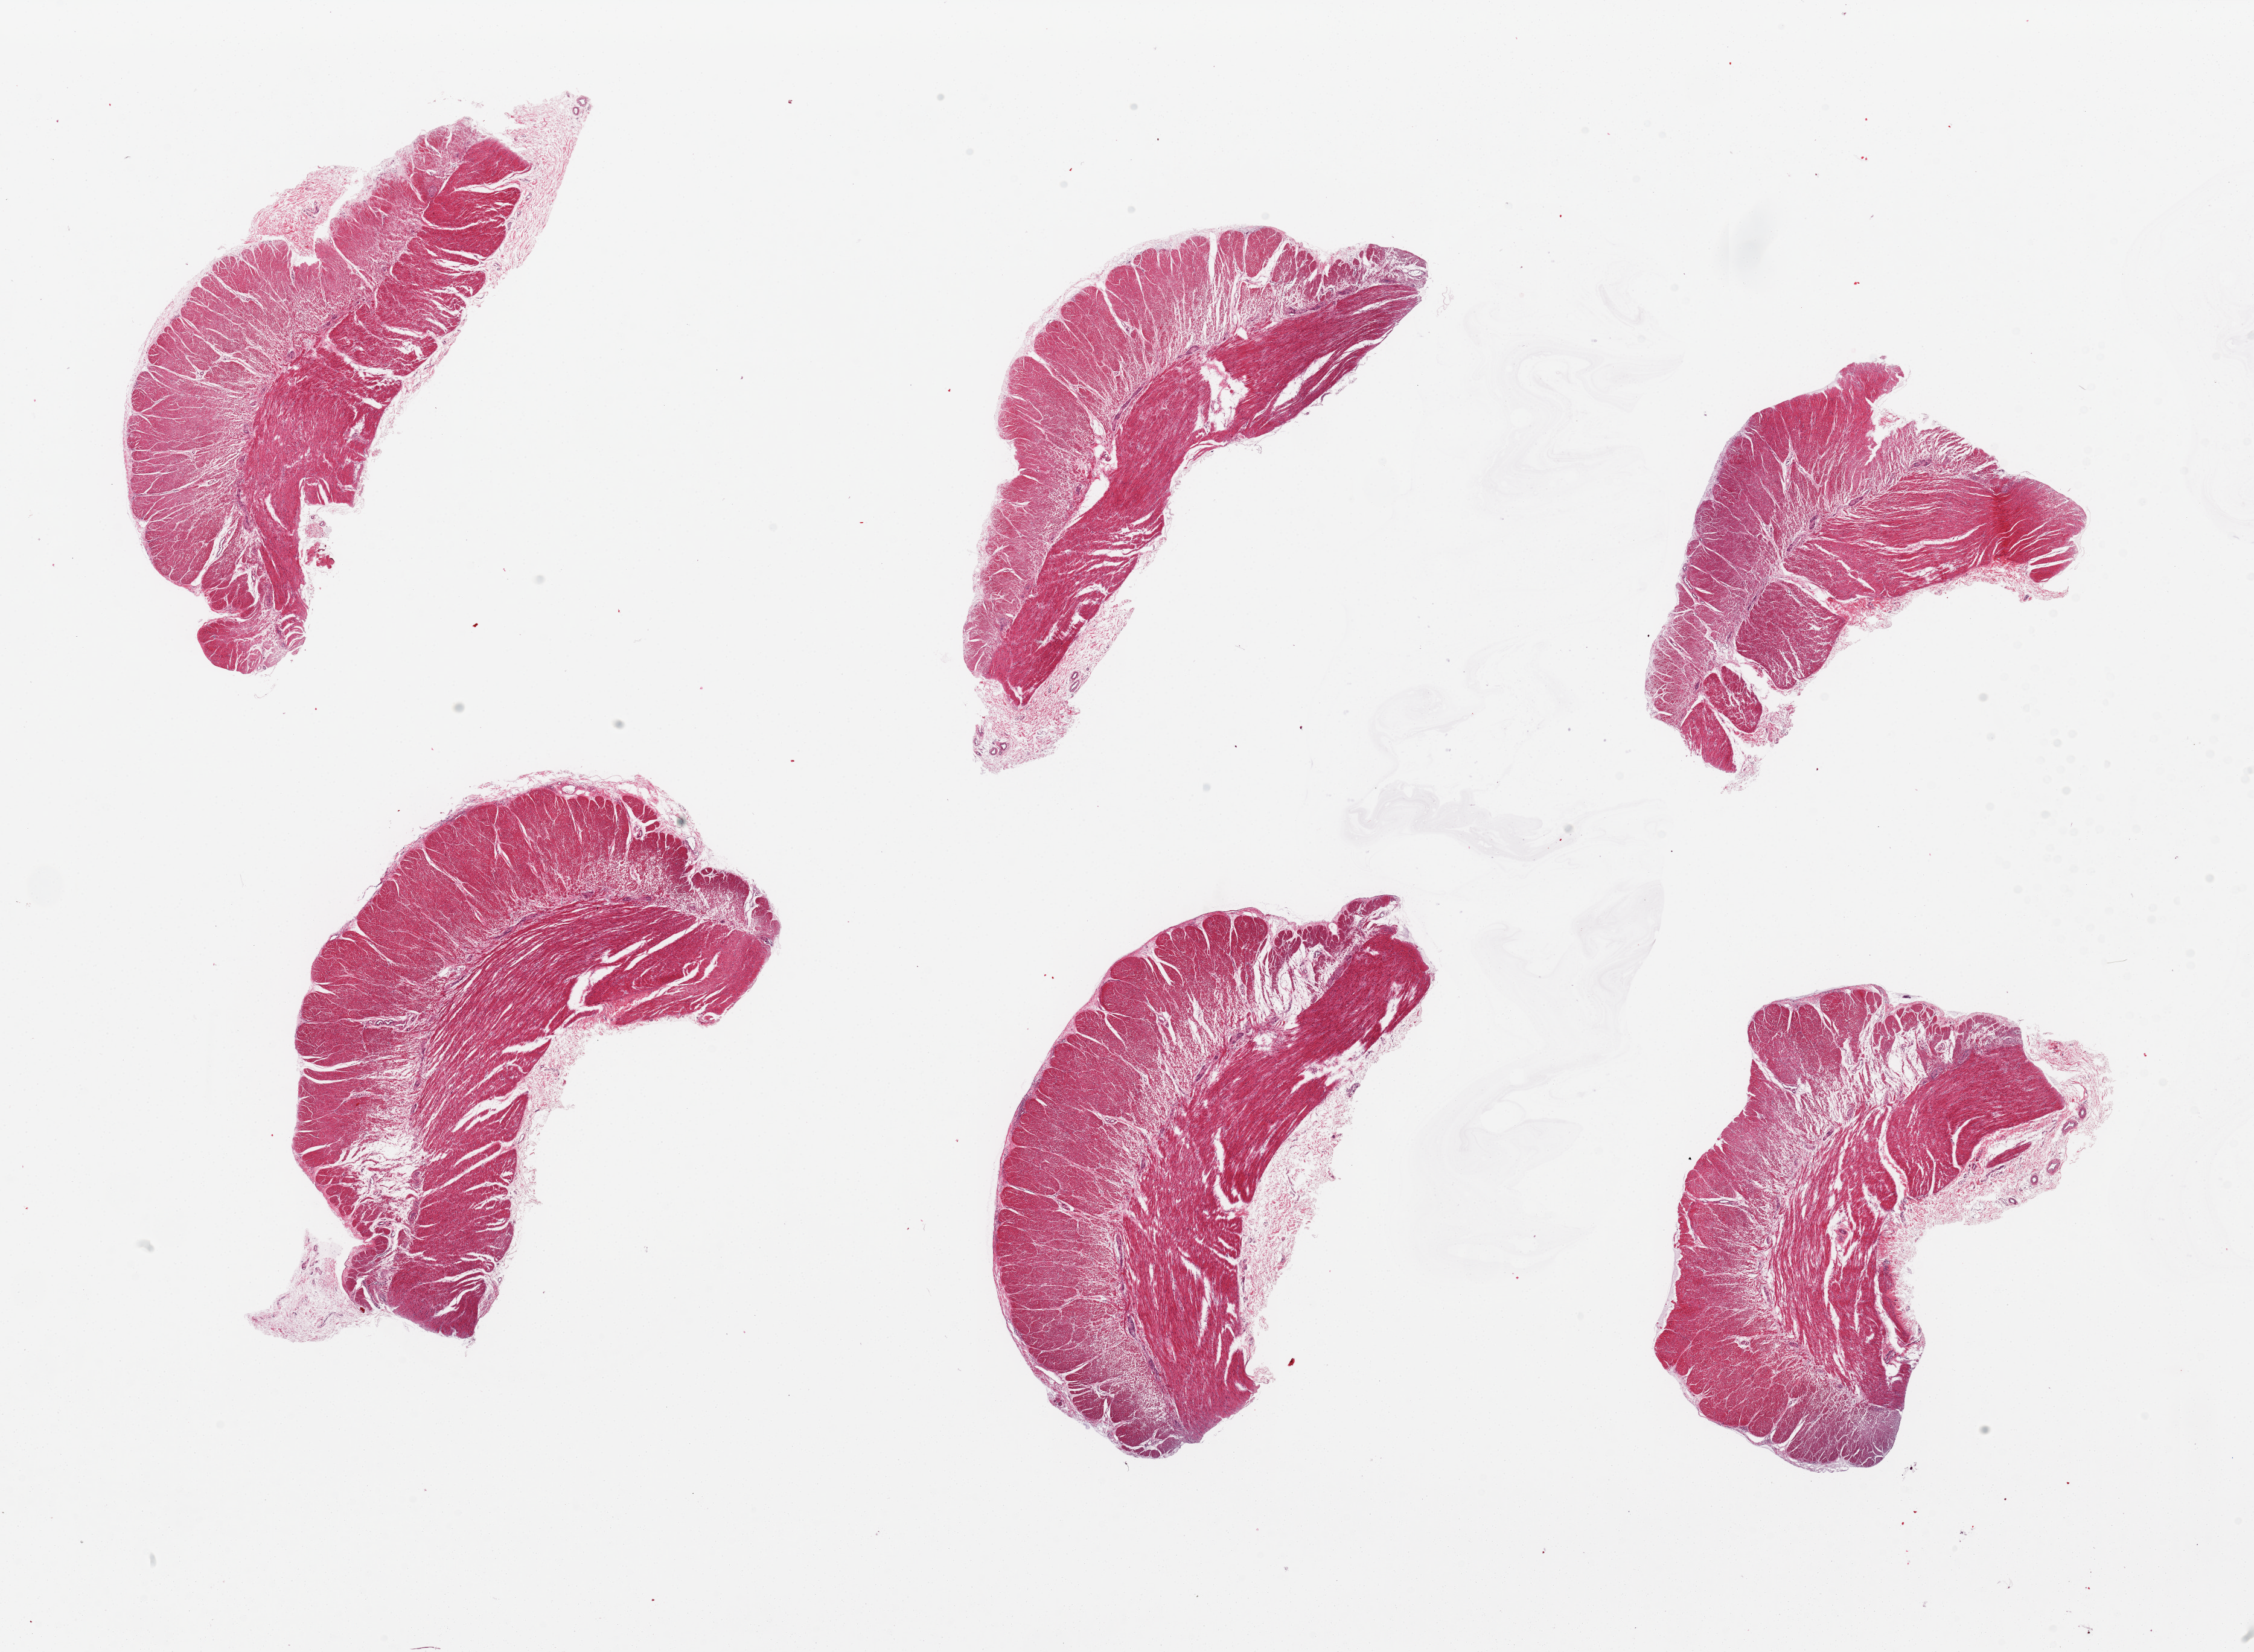
Digitized H&E-stained section — shown as a low-resolution overview of the whole scanned area (about 29.5 x 21.6 mm), PAXgene-fixed paraffin-embedded (PFPE) section, target tissue: sigmoid colon, donor tissue sample. Donor sex: male.
* pathologist's review note for this sample: 6 pieces, all muscularis, trace serosa, good specimens